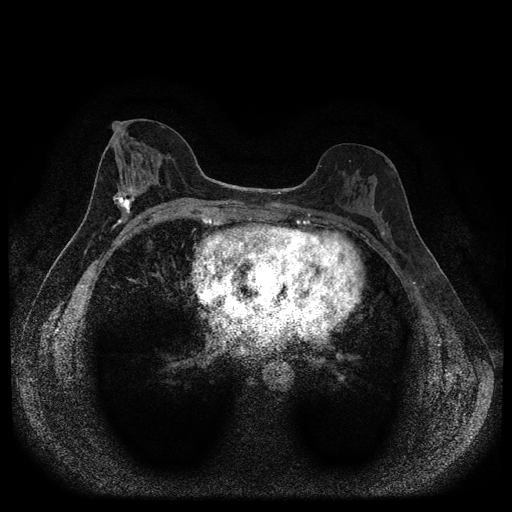
Breast MRI (dynamic contrast-enhanced, multi-phase), one axial slice. Slice 47 of 116 in the series (ordered by position). Dynamic contrast-enhanced series, time point 2 of 5 at this slice position (early post-contrast). 1.5 T. TE 2.7 ms, TR 5.4 ms. 2 mm slice thickness. 512 × 512 image matrix. Patient: female, 49 years.
Outlined on this slice (semi-automatically segmented with operator editing):
- breast lesion (labelled 'tumour' in the annotation; benign lesions carry a separate 'benign' label): bounding box [x1, y1, x2, y2] px = [112, 181, 138, 218]